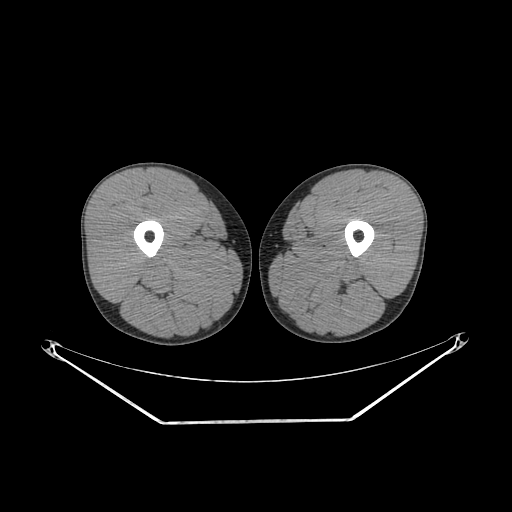
CT of an extremity soft-tissue mass (from a PET/CT study), one axial slice; position 228 of 267 along the scan axis; reconstruction kernel SOFT; 140 kVp; soft-tissue window (W 400 / L 40 HU); 3.75 mm slice thickness; 512 × 512 image matrix. Male patient. From the clinical record (not read from this slice): histological type: extraskeletal osteosarcoma; grade: high; site of the primary tumour: left adductur.
Annotated regions visible in this slice (expert contour drawn on MRI and transferred to this co-registered scan by the dataset authors):
- gross tumour volume (mass): box from (x=272, y=247) to (x=369, y=311) px